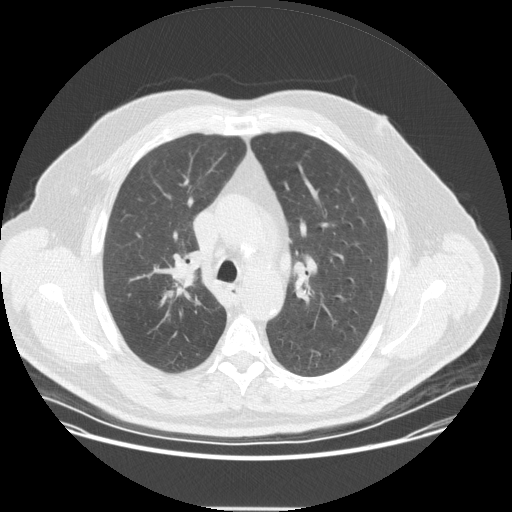
Low-dose screening chest CT, one axial slice. Slice 236 of 351 in the series (ordered by position). Lung window (W 1500 / L -600 HU). 512 × 512 image matrix, field of view 419 × 419 mm.
Annotated regions visible in this slice (manually delineated by an expert):
- lesion 1 (tumor, upper lobe of right lung): box from (x=168, y=266) to (x=198, y=288) px